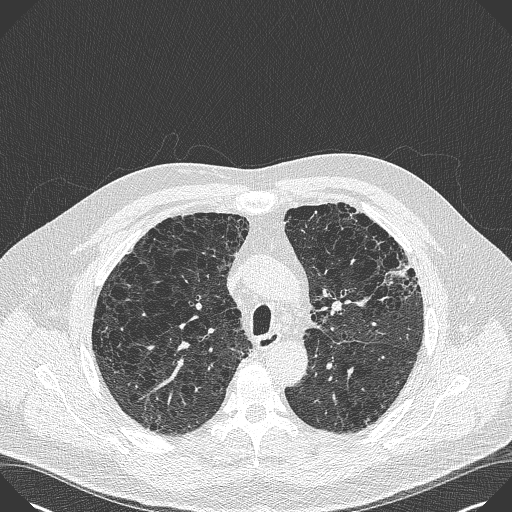
Axial slice from a low-dose chest CT screening exam, baseline annual screen, lung window (W 1500 / L -600 HU), 1 mm slice thickness, lung (sharp) reconstruction kernel (B50f), slice 121 of 383 in the series. Male, age 59 years at enrolment. Current smoker at enrolment.
• Lesion marked by an expert reader, box from (x=375, y=240) to (x=427, y=291) px.
• Screening reader's record for this exam: no non-calcified nodule ≥4 mm recorded.
• Official screen result: negative screen, minor abnormalities not suspicious for lung cancer.
• Later outcome: lung cancer diagnosed 909 days after this screen (after the third annual screen) — bronchiolo-alveolar carcinoma, mixed mucinous and non-mucinous, left upper lobe, stage IA (AJCC 6th edition), 20 mm at pathology.